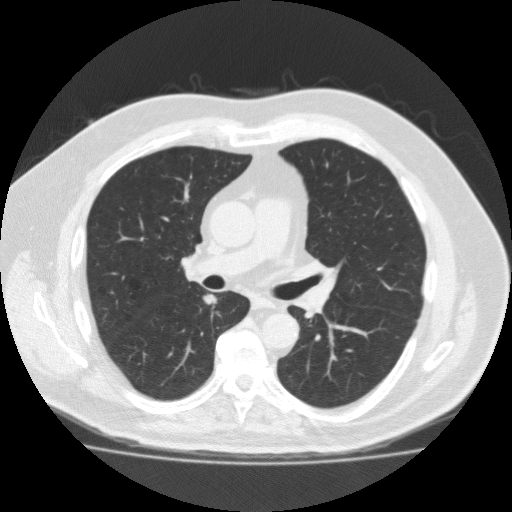
Axial slice from a low-dose chest CT screening exam. Third screening round (two years after baseline). Lung window (W 1500 / L -600 HU). 120 kVp. 512 × 512 image matrix. Male participant, aged 56 years at enrolment.
Lesion marked by an expert reader, bounding box <187,281,232,318> (left, top, right, bottom; pixels). Reader record for this screening exam (exam-level; its link to the box is not recorded): non-calcified nodule or mass ≥4 mm, right lower lobe, 12 × 8 mm, spiculated (stellate) margins, soft tissue attenuation, pre-existing on the prior screen: yes; interval growth: yes. Lung cancer was diagnosed 49 days after this screen: adenocarcinoma, NOS, right lower lobe, moderately differentiated (G2), stage IA (AJCC 6th edition), 12 mm at pathology.